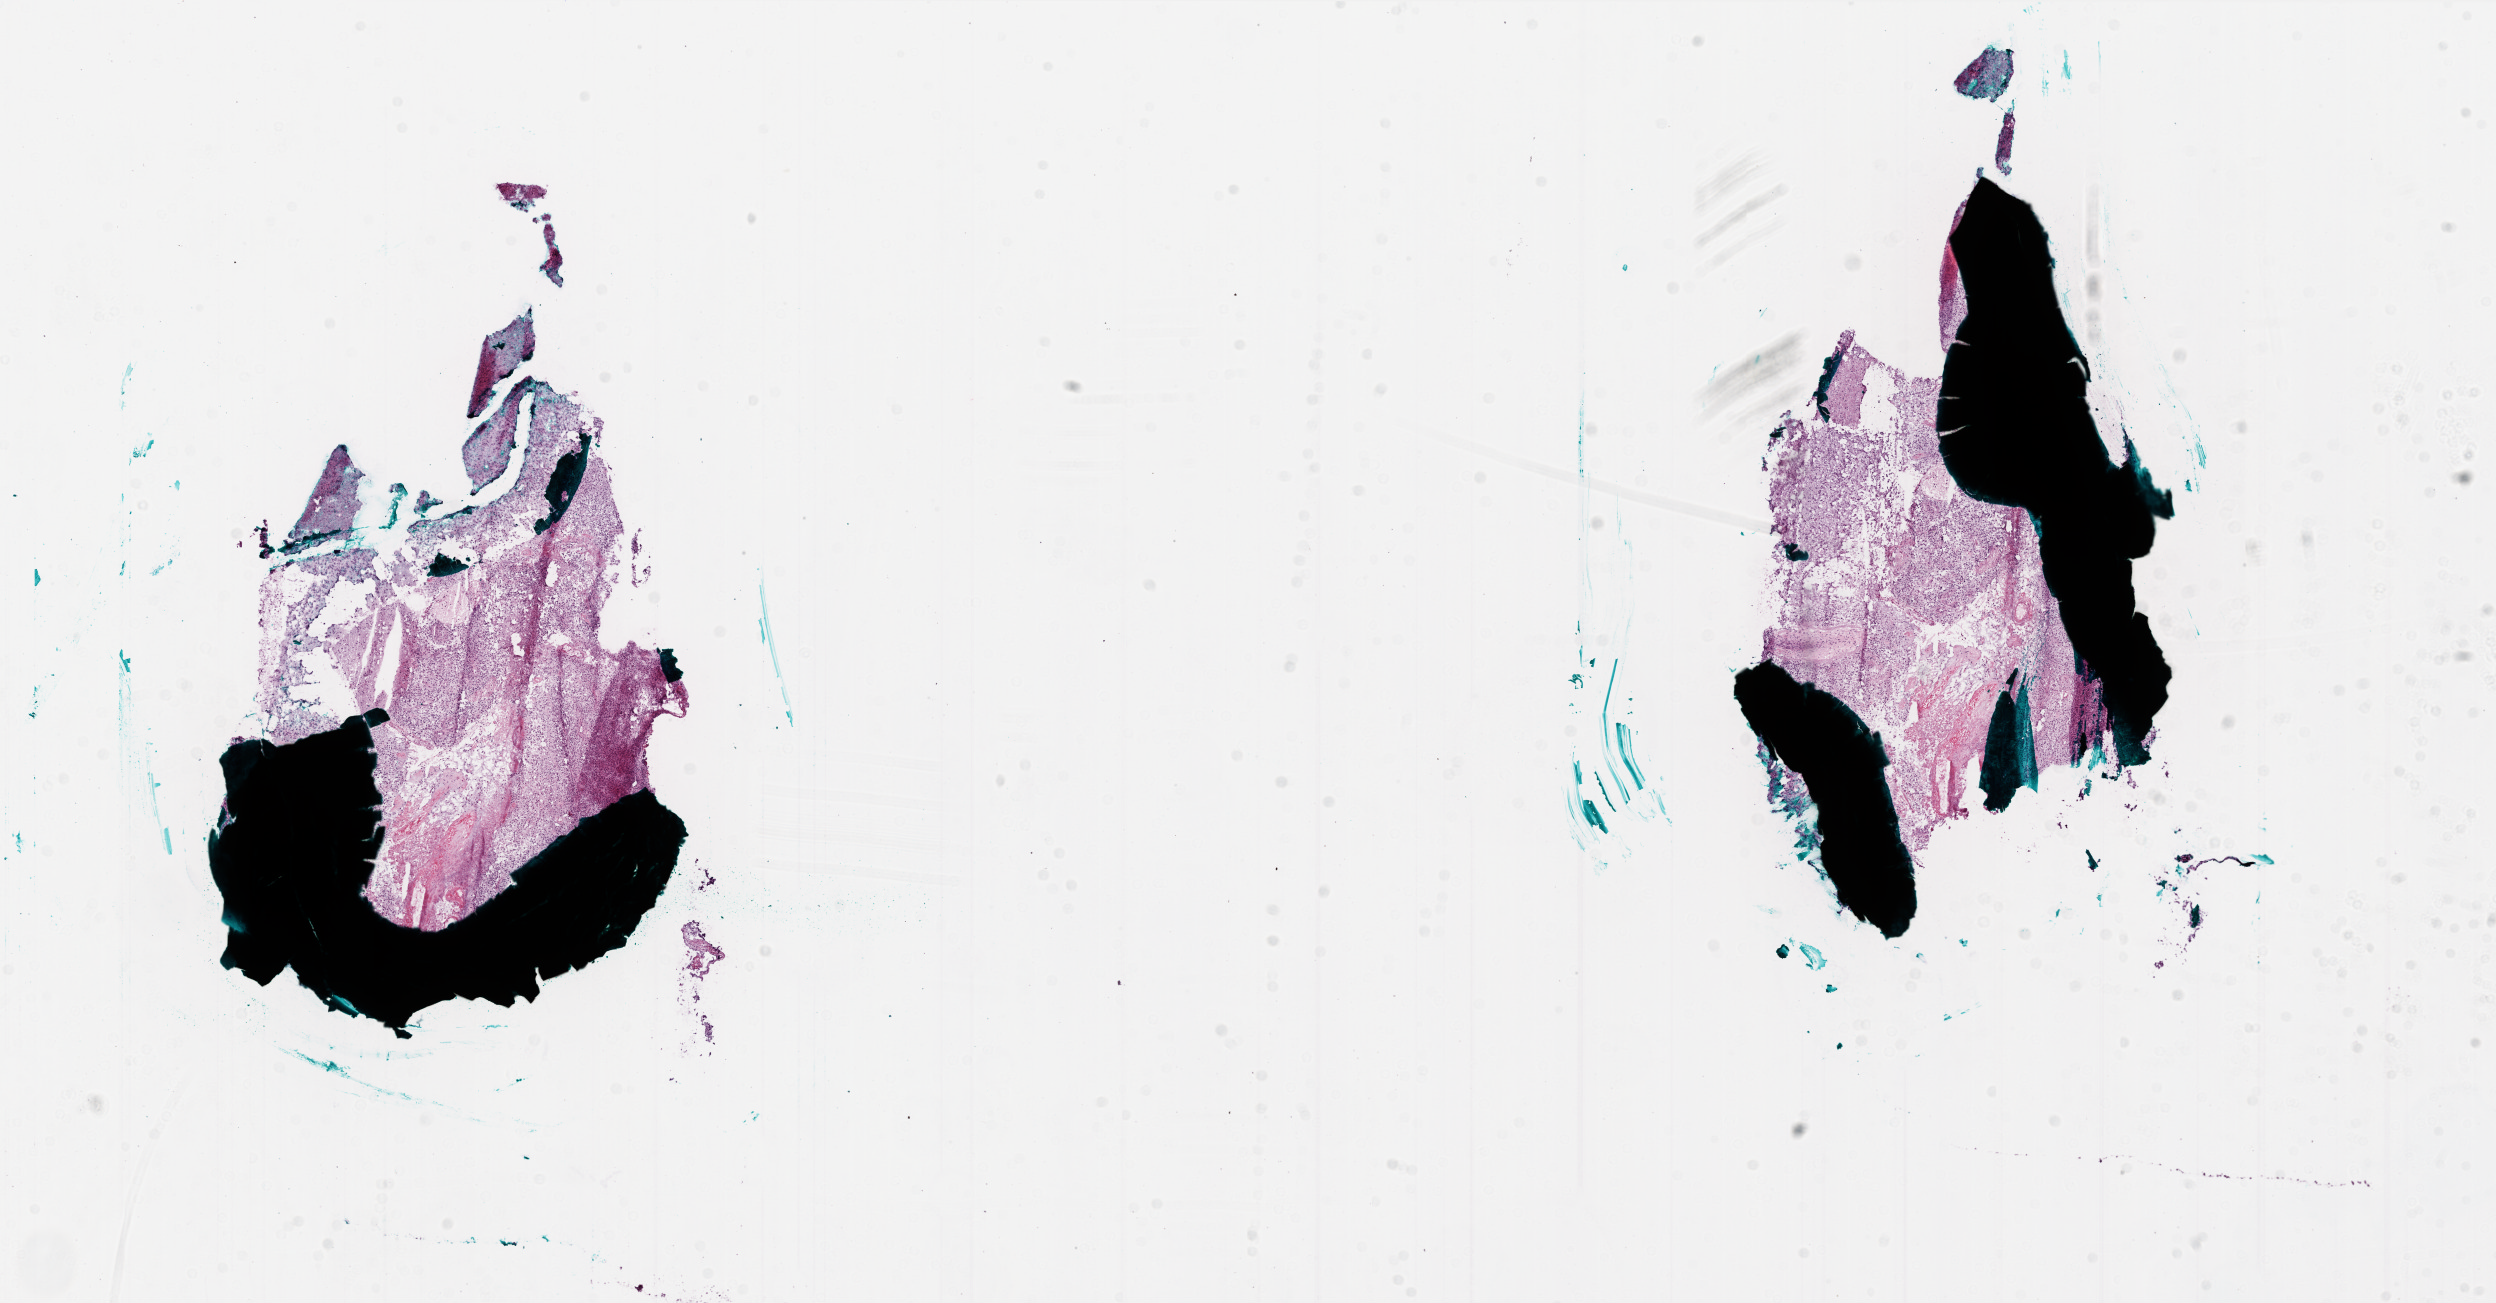
Digitized H&E tissue section (whole slide) — shown as a low-resolution overview of the whole scanned area (about 20.0 x 10.4 mm, from a 20x scan); frozen section; brain, primary tumour sample. Male, age 65 years at initial diagnosis. Composition of this section per pathologist review: tumour cells 75%, tumour nuclei 95%, normal cells 0%, stromal cells 15%, necrosis 10%.
Pathologic diagnosis: Glioblastoma.